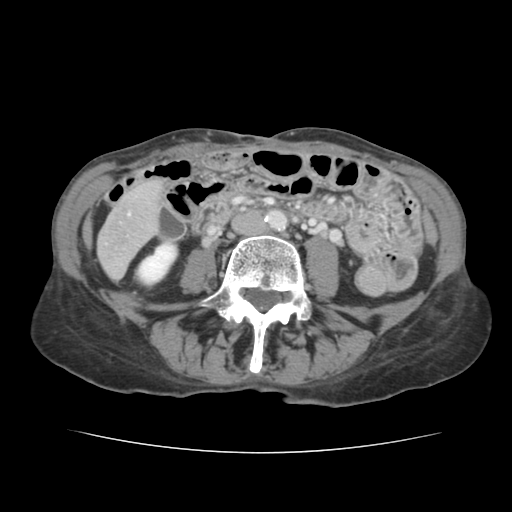
Contrast-enhanced abdominal CT, one axial slice; position 23 of 136 along the scan axis; 120 kVp; intravenous contrast given; soft-tissue window (W 400 / L 40 HU); 2.5 mm slice thickness; 512 × 512 image matrix, field of view 319 × 319 mm. Female patient, age 77 years. Case-level facts recorded for this patient, not image findings: diagnosis: colorectal cancer liver metastases, imaged before liver resection; multiple liver metastases: yes.
Annotated regions visible in this slice (manually delineated by an expert):
- liver: bounding box (x1, y1, x2, y2) in pixels: (99, 183, 161, 278)